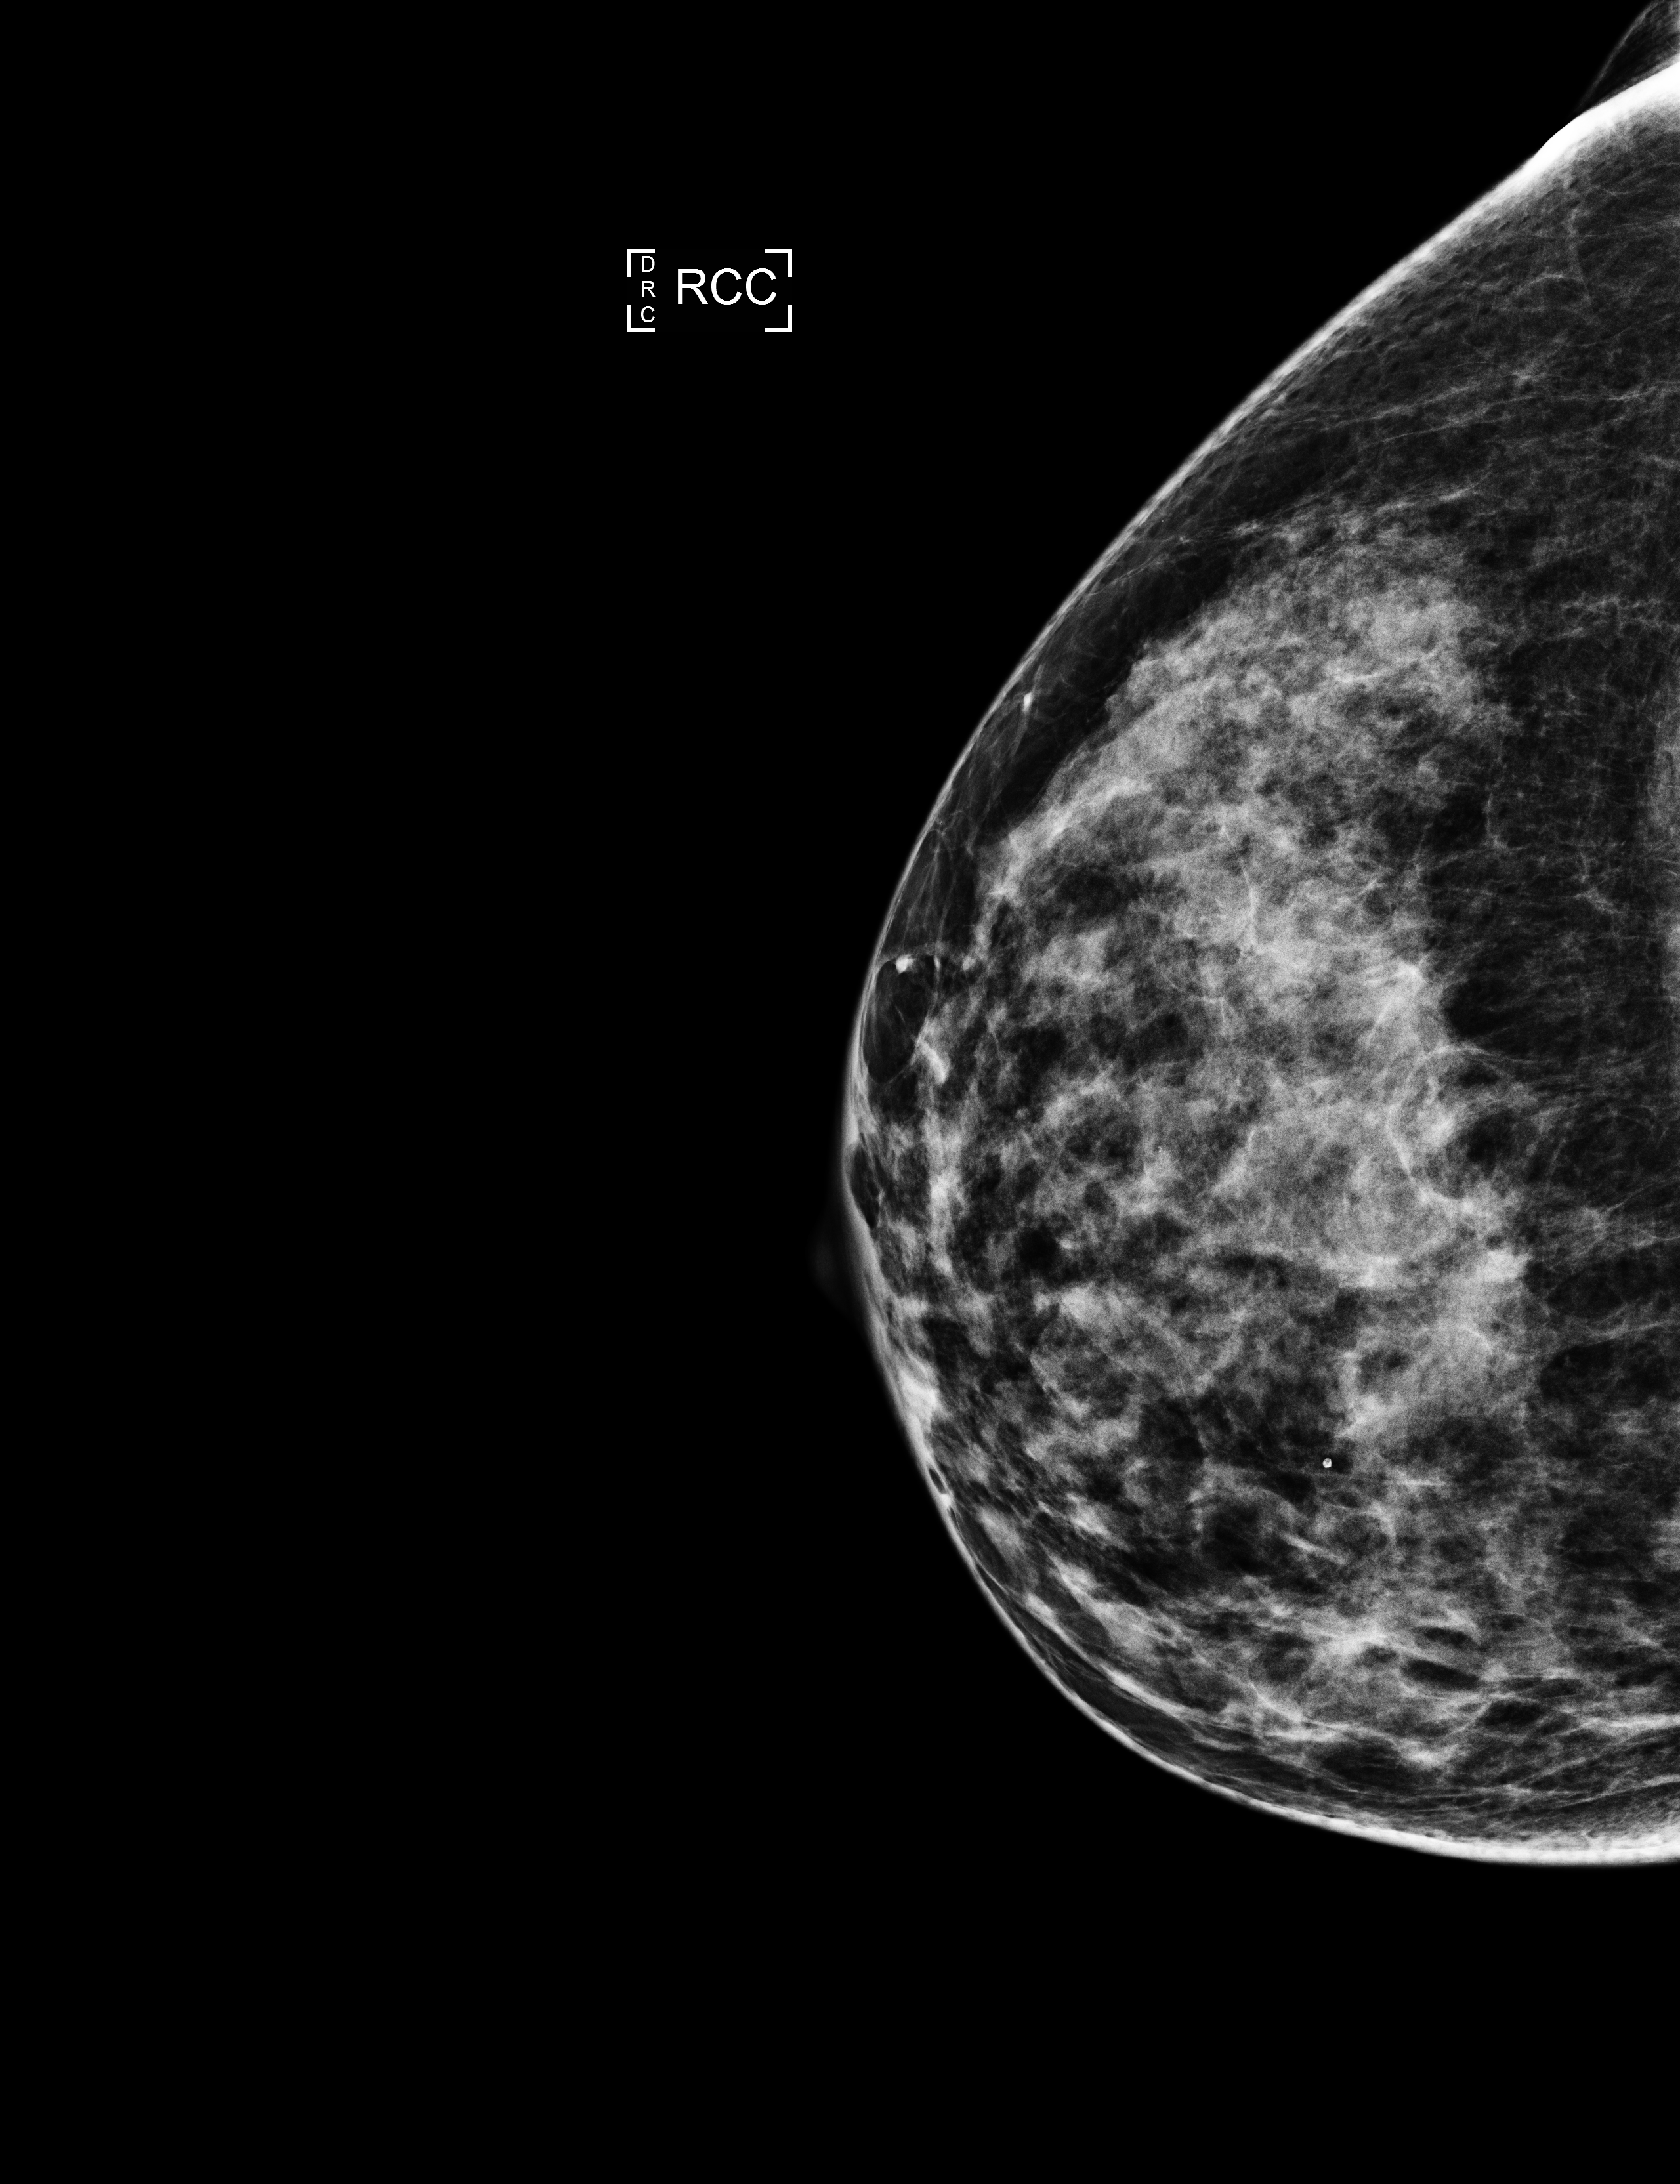
Full-field digital mammogram (FFDM); right breast; CC view; screening examination. Female patient, age 60 years.
Final BI-RADS assessment for this screening round (tomosynthesis exam, both breasts): category 1.